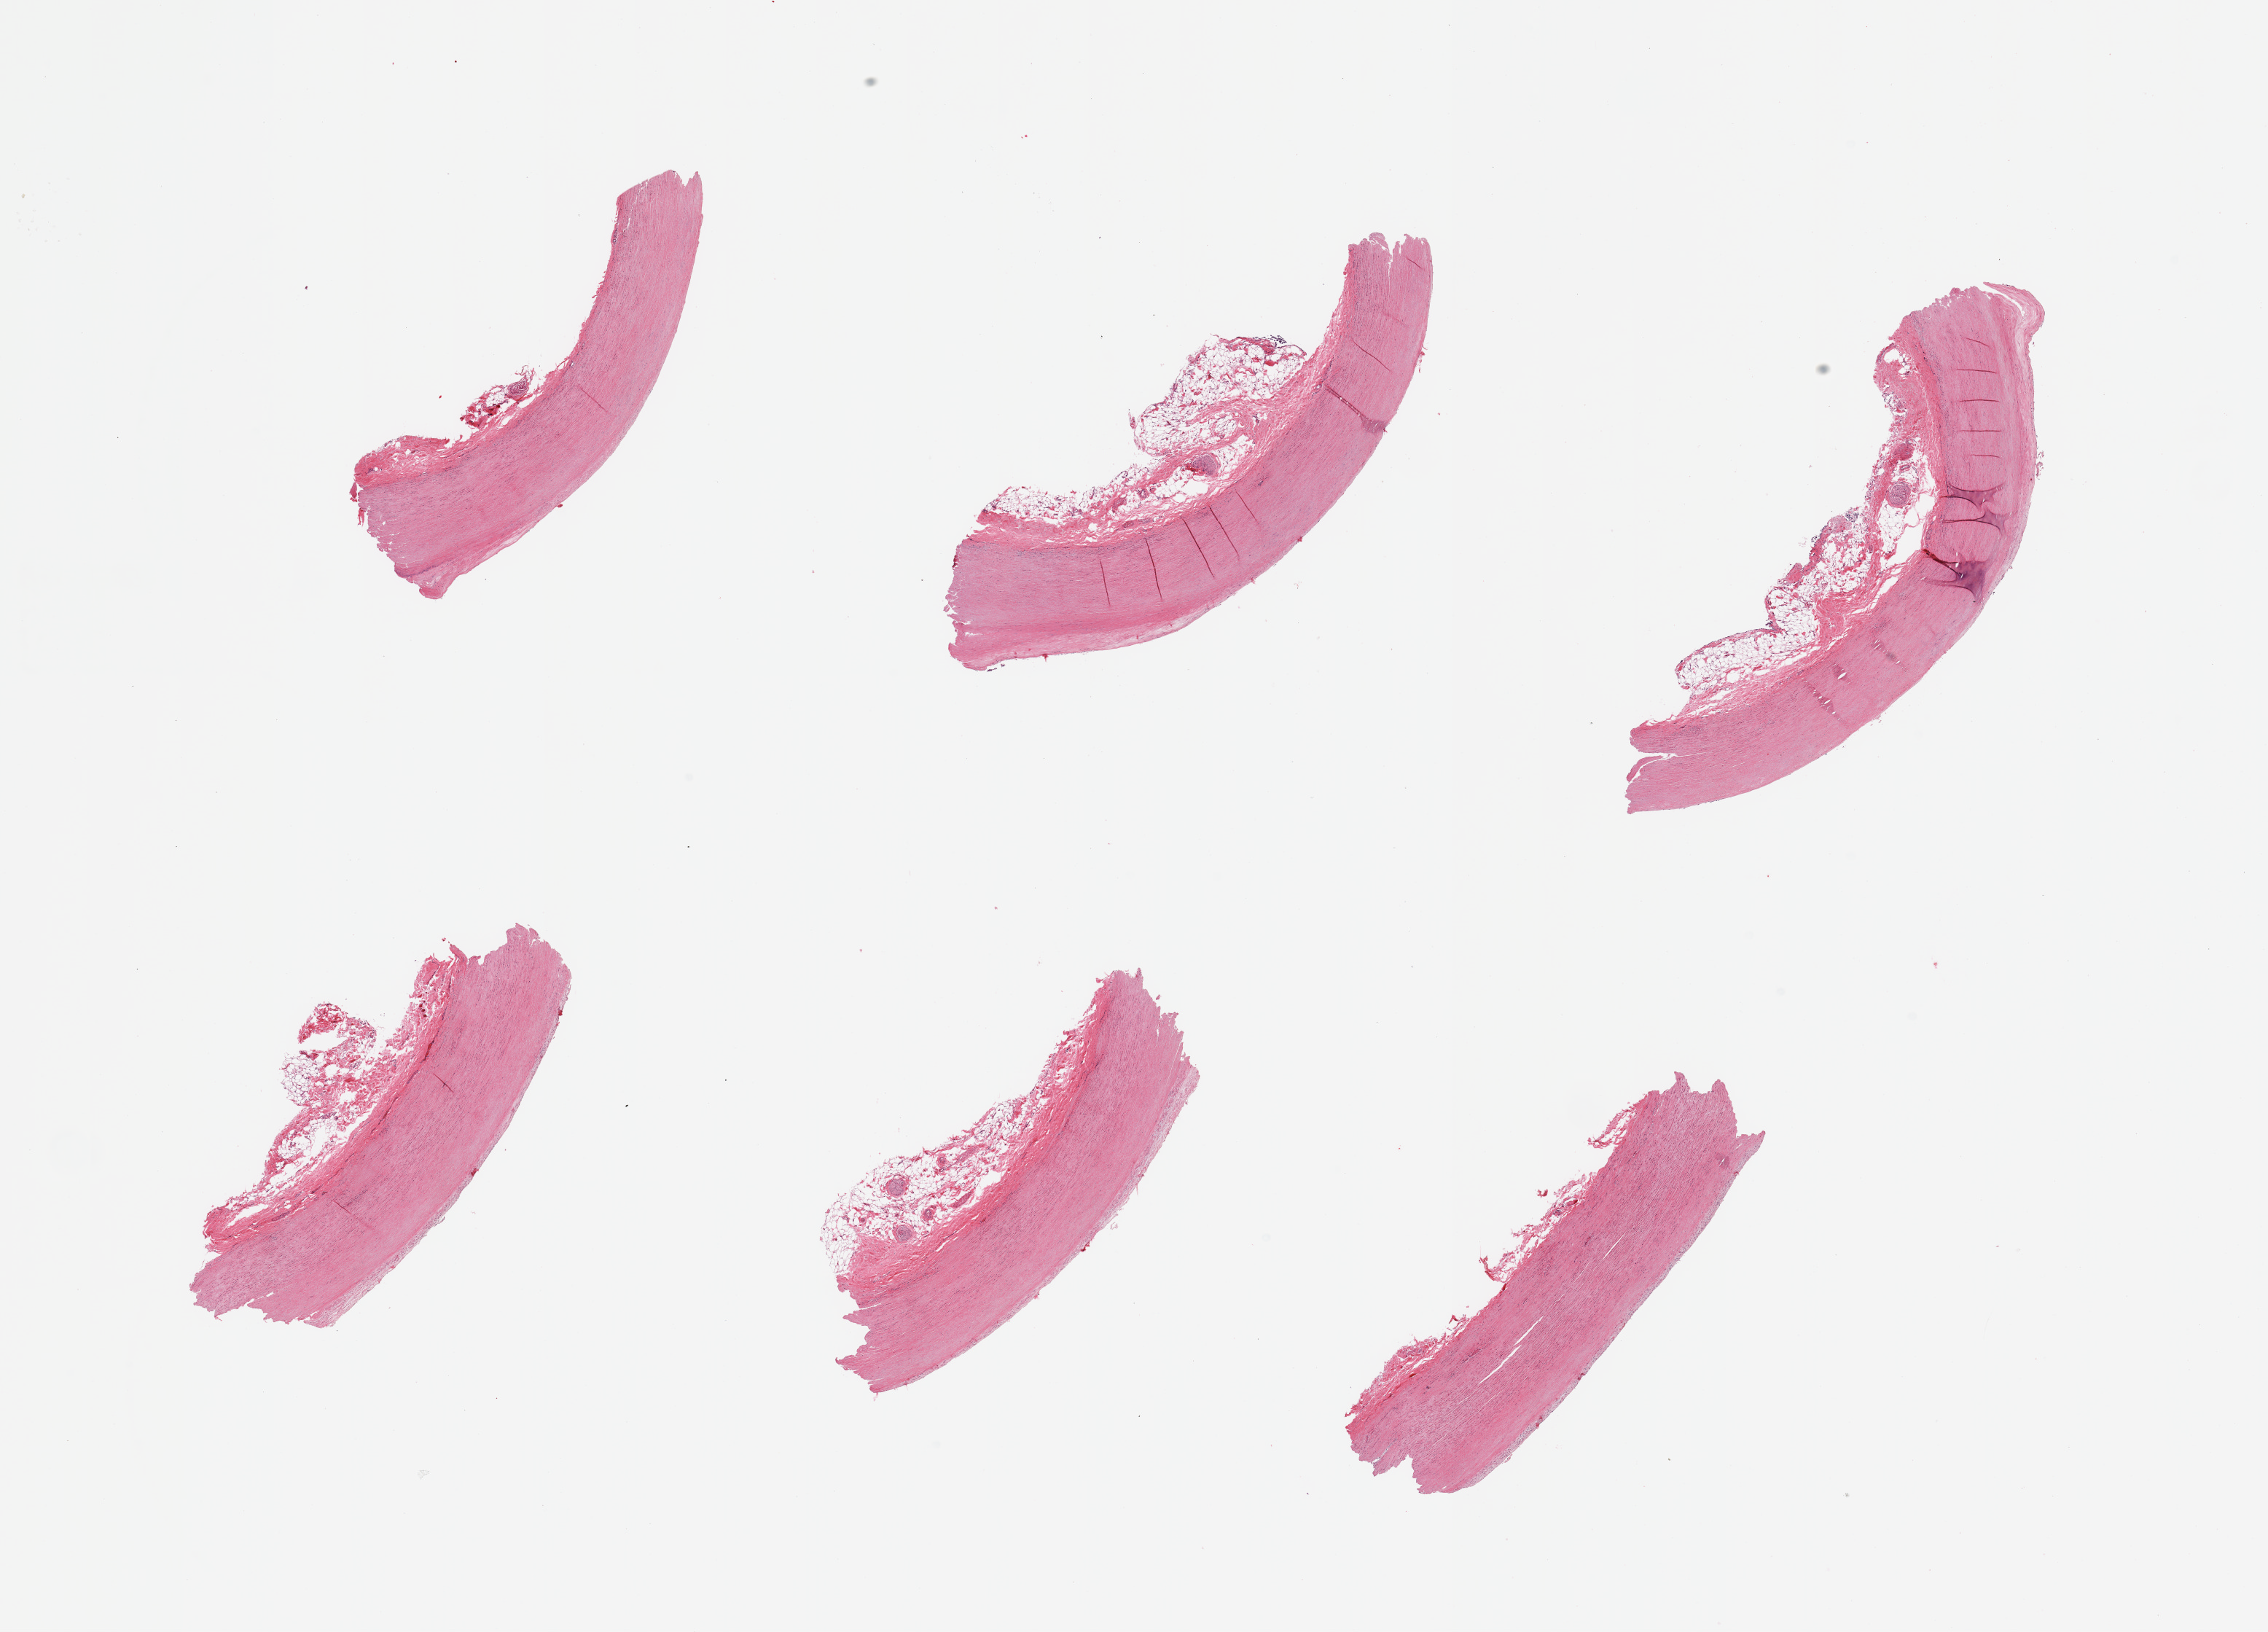
Digitized H&E-stained section, low-resolution overview of the scanned area, about 24.6 x 17.7 mm, PAXgene-fixed, paraffin-embedded tissue, sampled site (target tissue): aorta, tissue donor sample. Male donor.
* pathologist's review note for this sample: 6 pieces, atherosis up to ~0.2mm